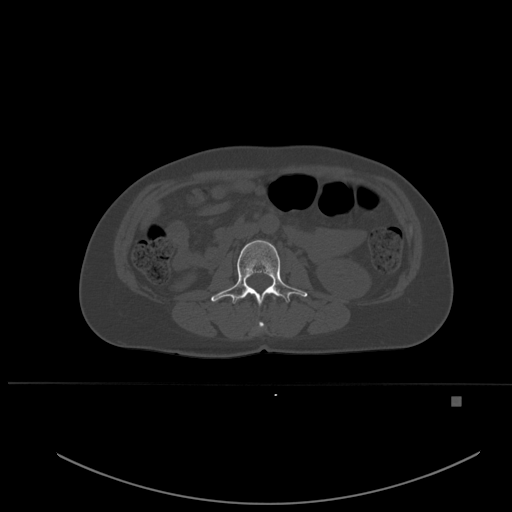
CT including the spine, one axial slice; position 215 of 651 along the scan axis; bone window (W 1800 / L 400 HU); 1.5 mm slice thickness; 512 × 512 image matrix, field of view 443 × 443 mm. Female patient, age 49 years. From the clinical record (not read from this slice): primary cancer: breast; vertebrae with lytic lesions (as recorded): L3, T12, L4.
Structures marked on this image (semi-automatically segmented with operator editing):
- L1 vertebra: box from (x=259, y=297) to (x=276, y=328) px
- L2 vertebra: (x=211, y=240)–(x=308, y=305)